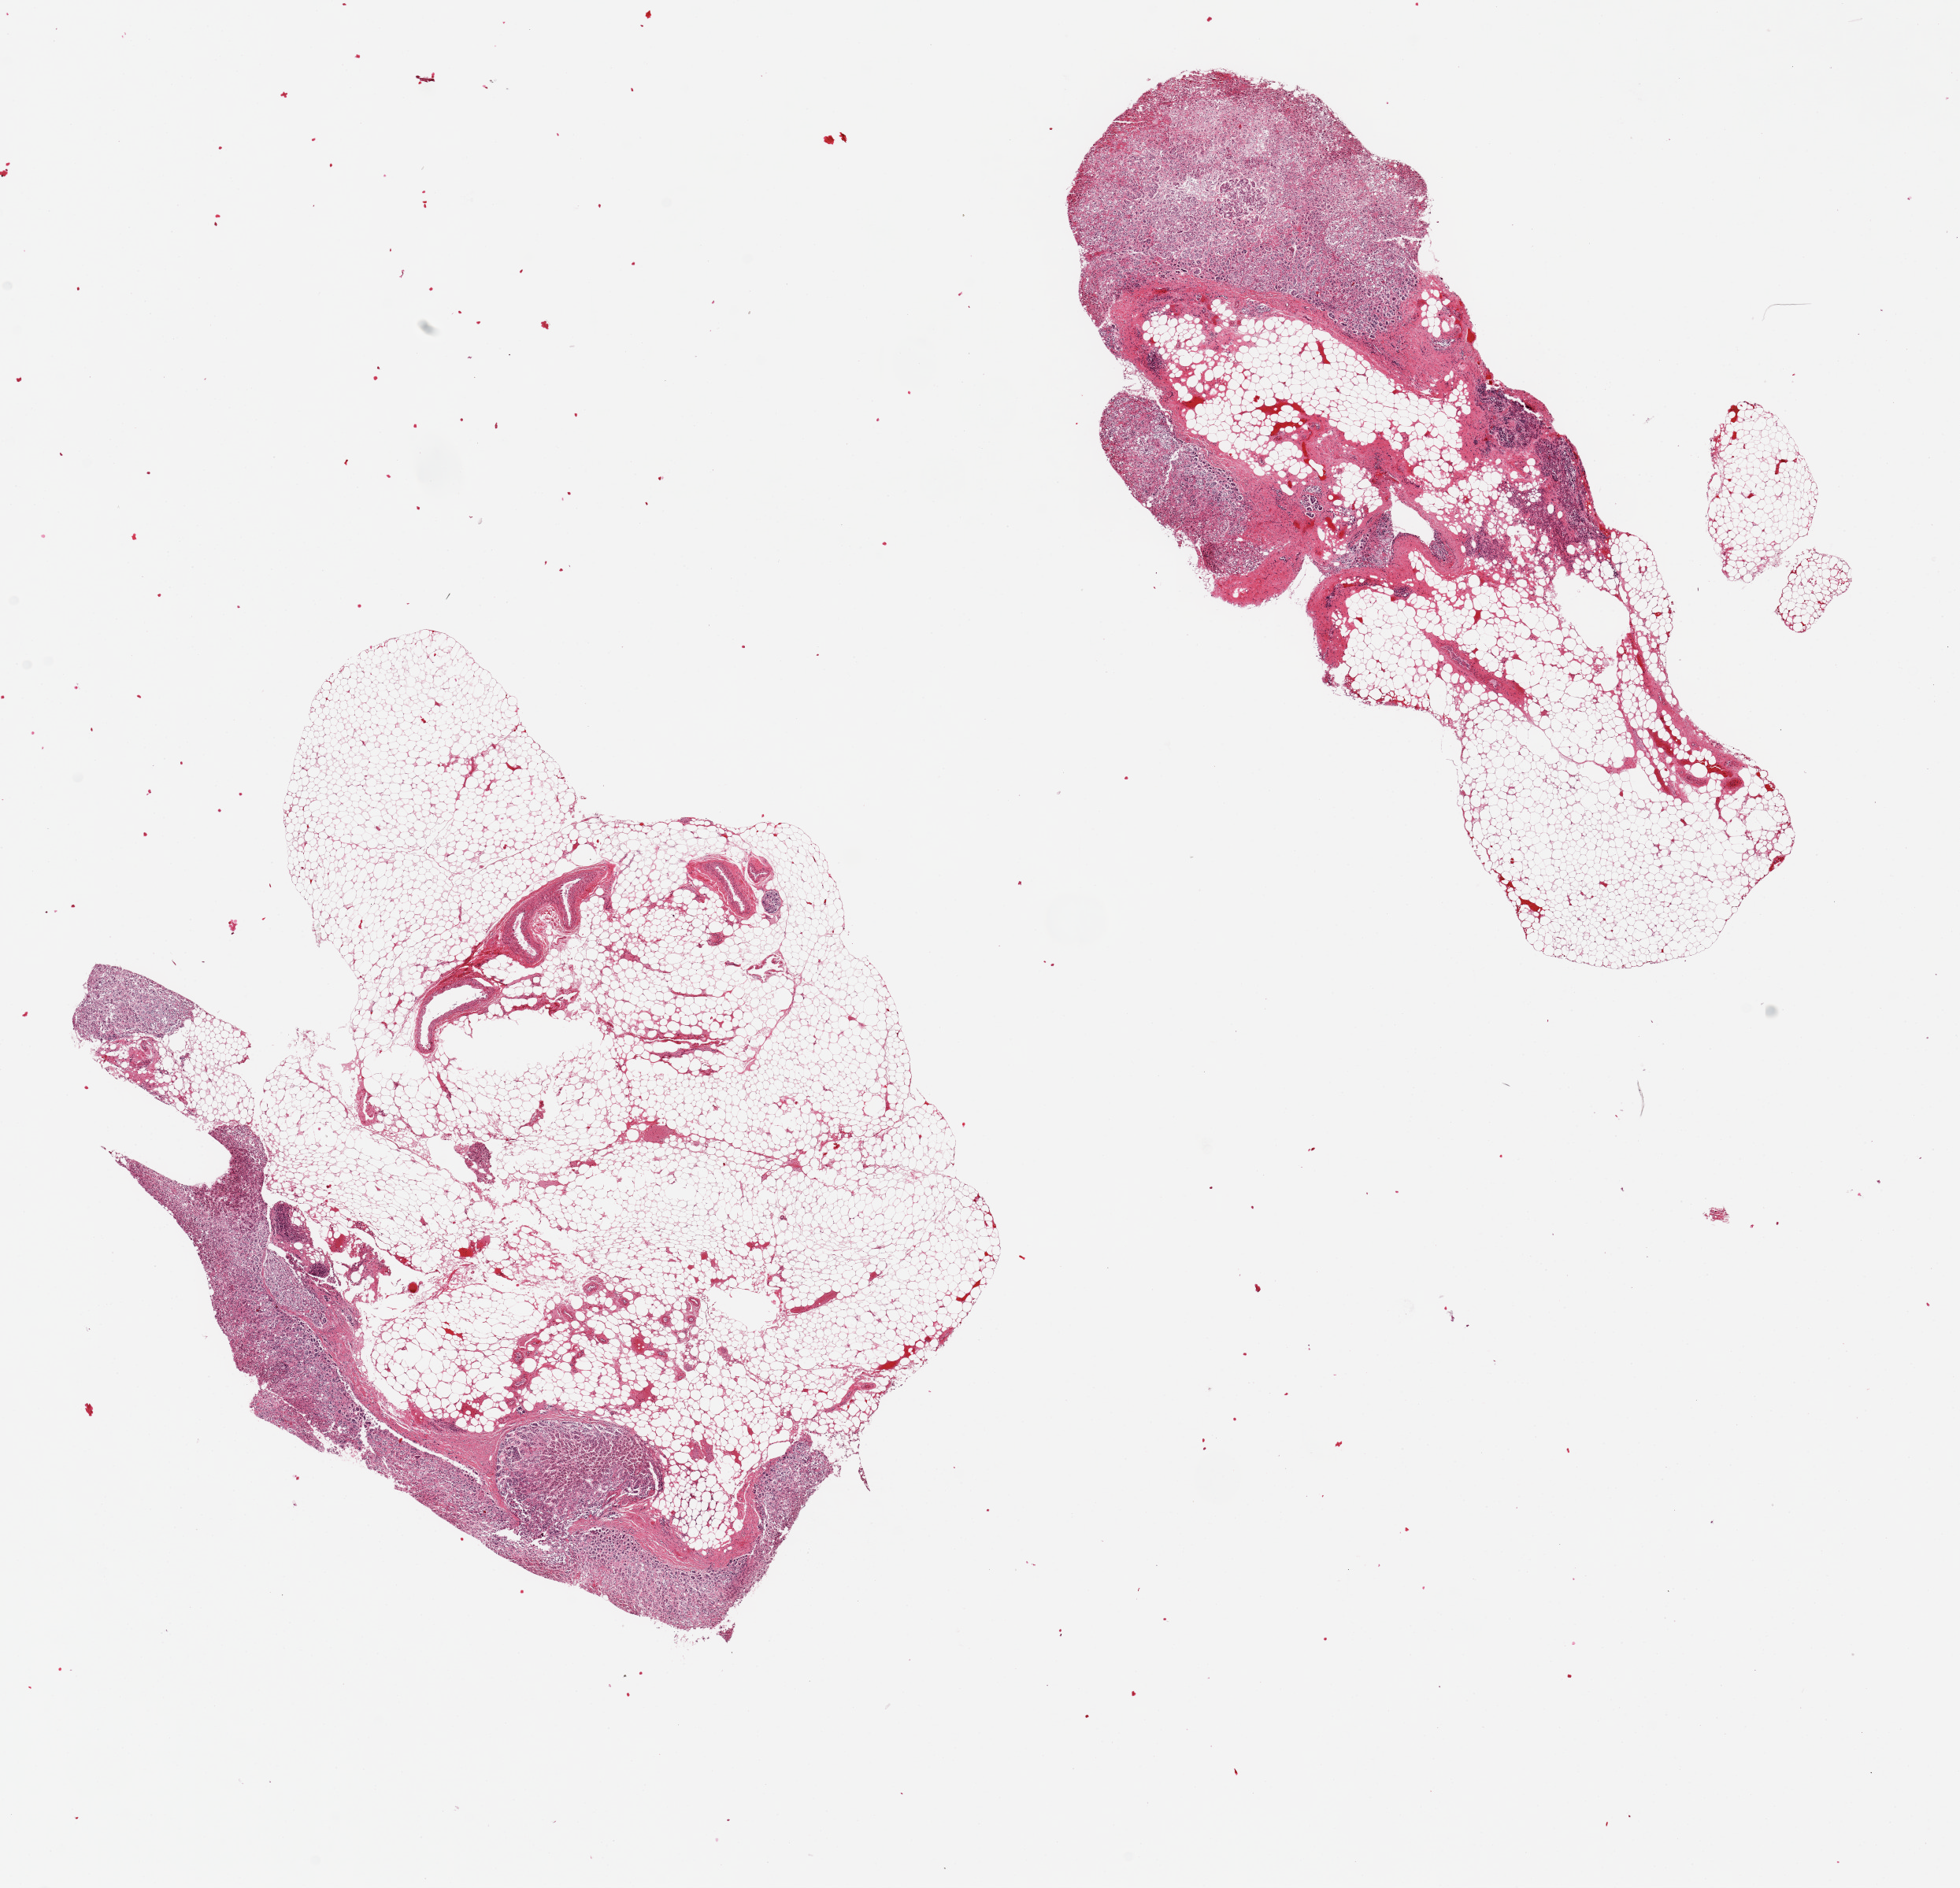
Haematoxylin and eosin whole-slide image — whole scanned area (about 19.7 x 19.0 mm) shown as a low-resolution overview, PAXgene-fixed paraffin-embedded (PFPE) section, section of adrenal gland (target tissue), tissue donor sample. Donor sex: female.
Pathologist's review note for this sample: 2 pieces, one with 80% other with 60% fat.